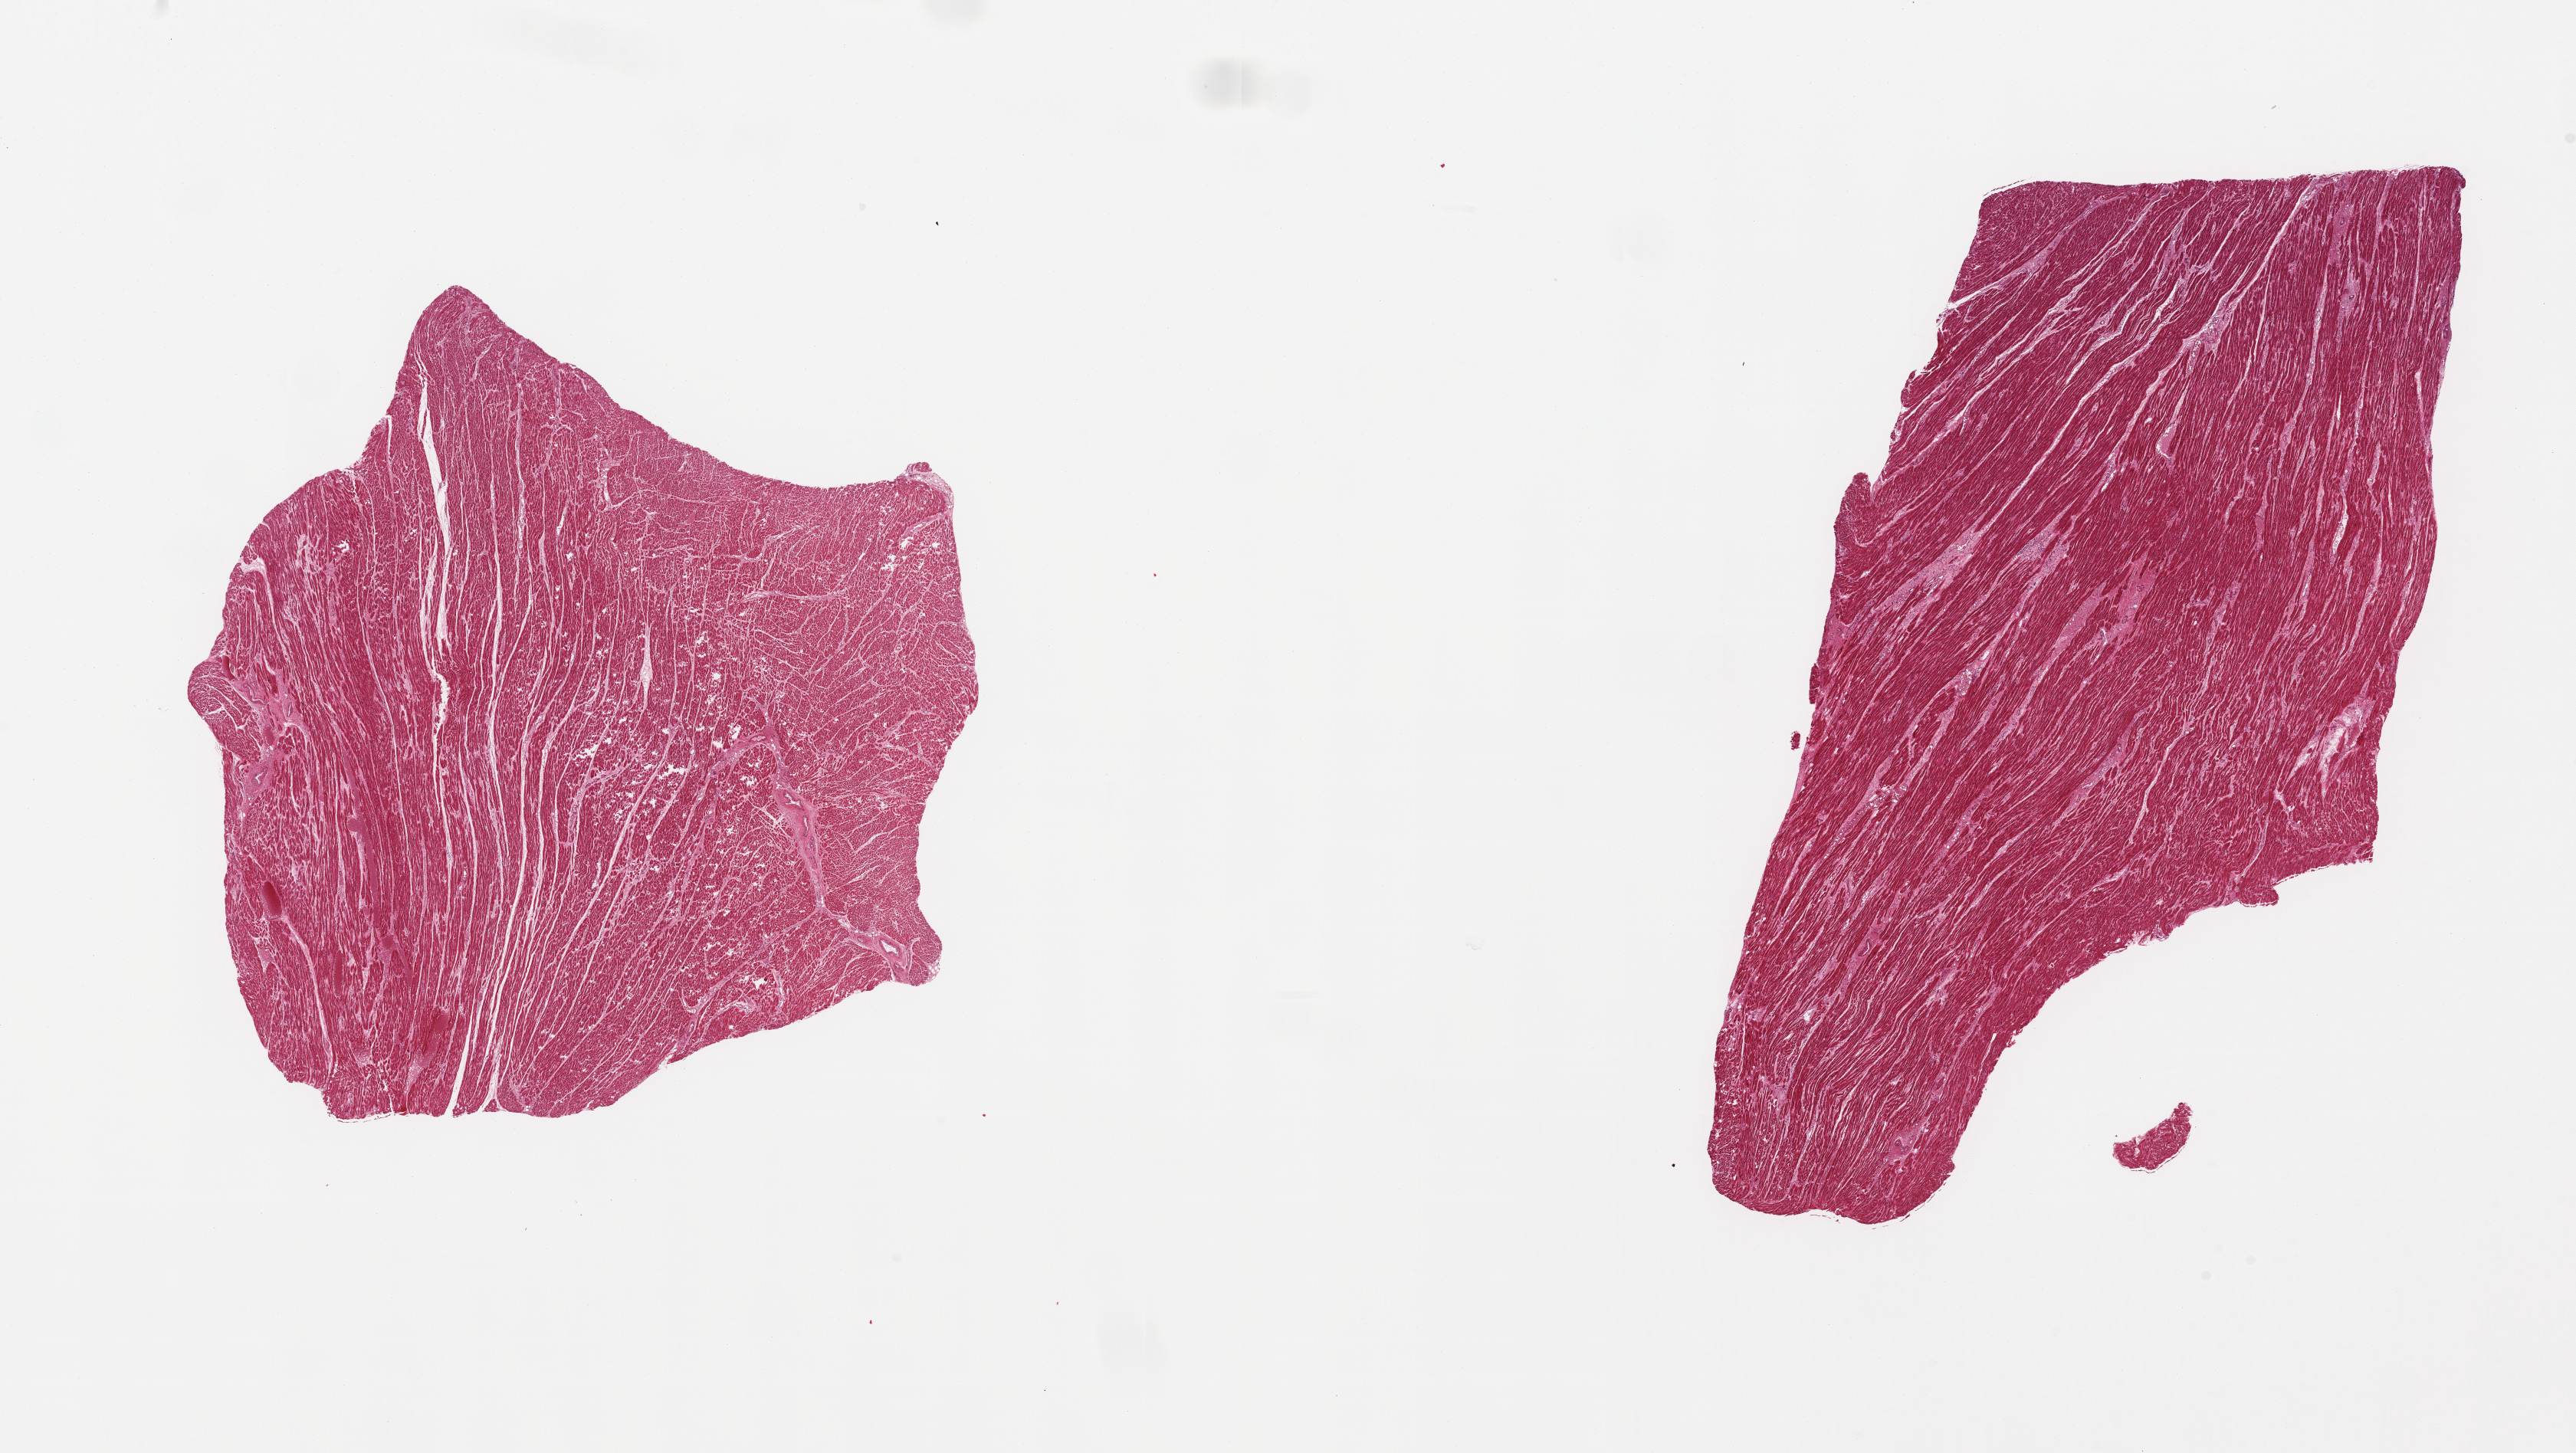
Whole-slide image, haematoxylin and eosin stain, a low-resolution overview of the entire scanned area, about 26.6 x 15.0 mm (acquisition: 20x scan). PAXgene-fixed paraffin-embedded (PFPE) section. Target tissue: heart. Tissue donor sample. Male donor.
Reviewer comment on this tissue sample: 2 pieces; in 1 piece a few foci of punched out myofibers, 1 with interstitial inflammatory cells and atrophic myofibers, consistent with scar from a healed infarct.